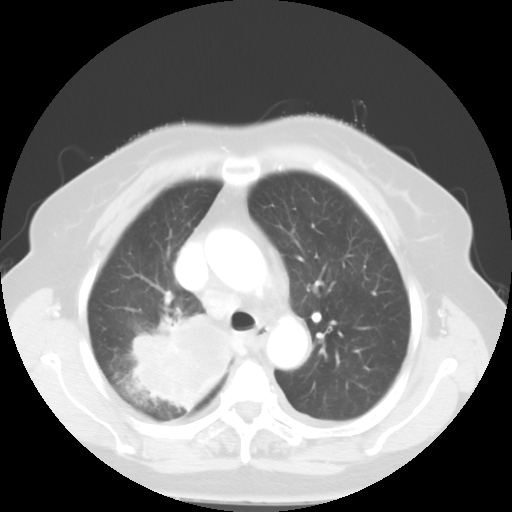
Chest CT, one axial slice; lung window (W 1500 / L -600 HU); 5 mm slice thickness; 512 × 512 image matrix. Patient: female, 81 years. Case-level facts recorded for this patient, not image findings: clinical TNM (as recorded): T4 N3 M1b.
Outlined on this slice (bounding box drawn by a radiologist):
- lung tumour (recorded histology: adenocarcinoma): bounding box (x1, y1, x2, y2) in pixels: (130, 309, 236, 414)